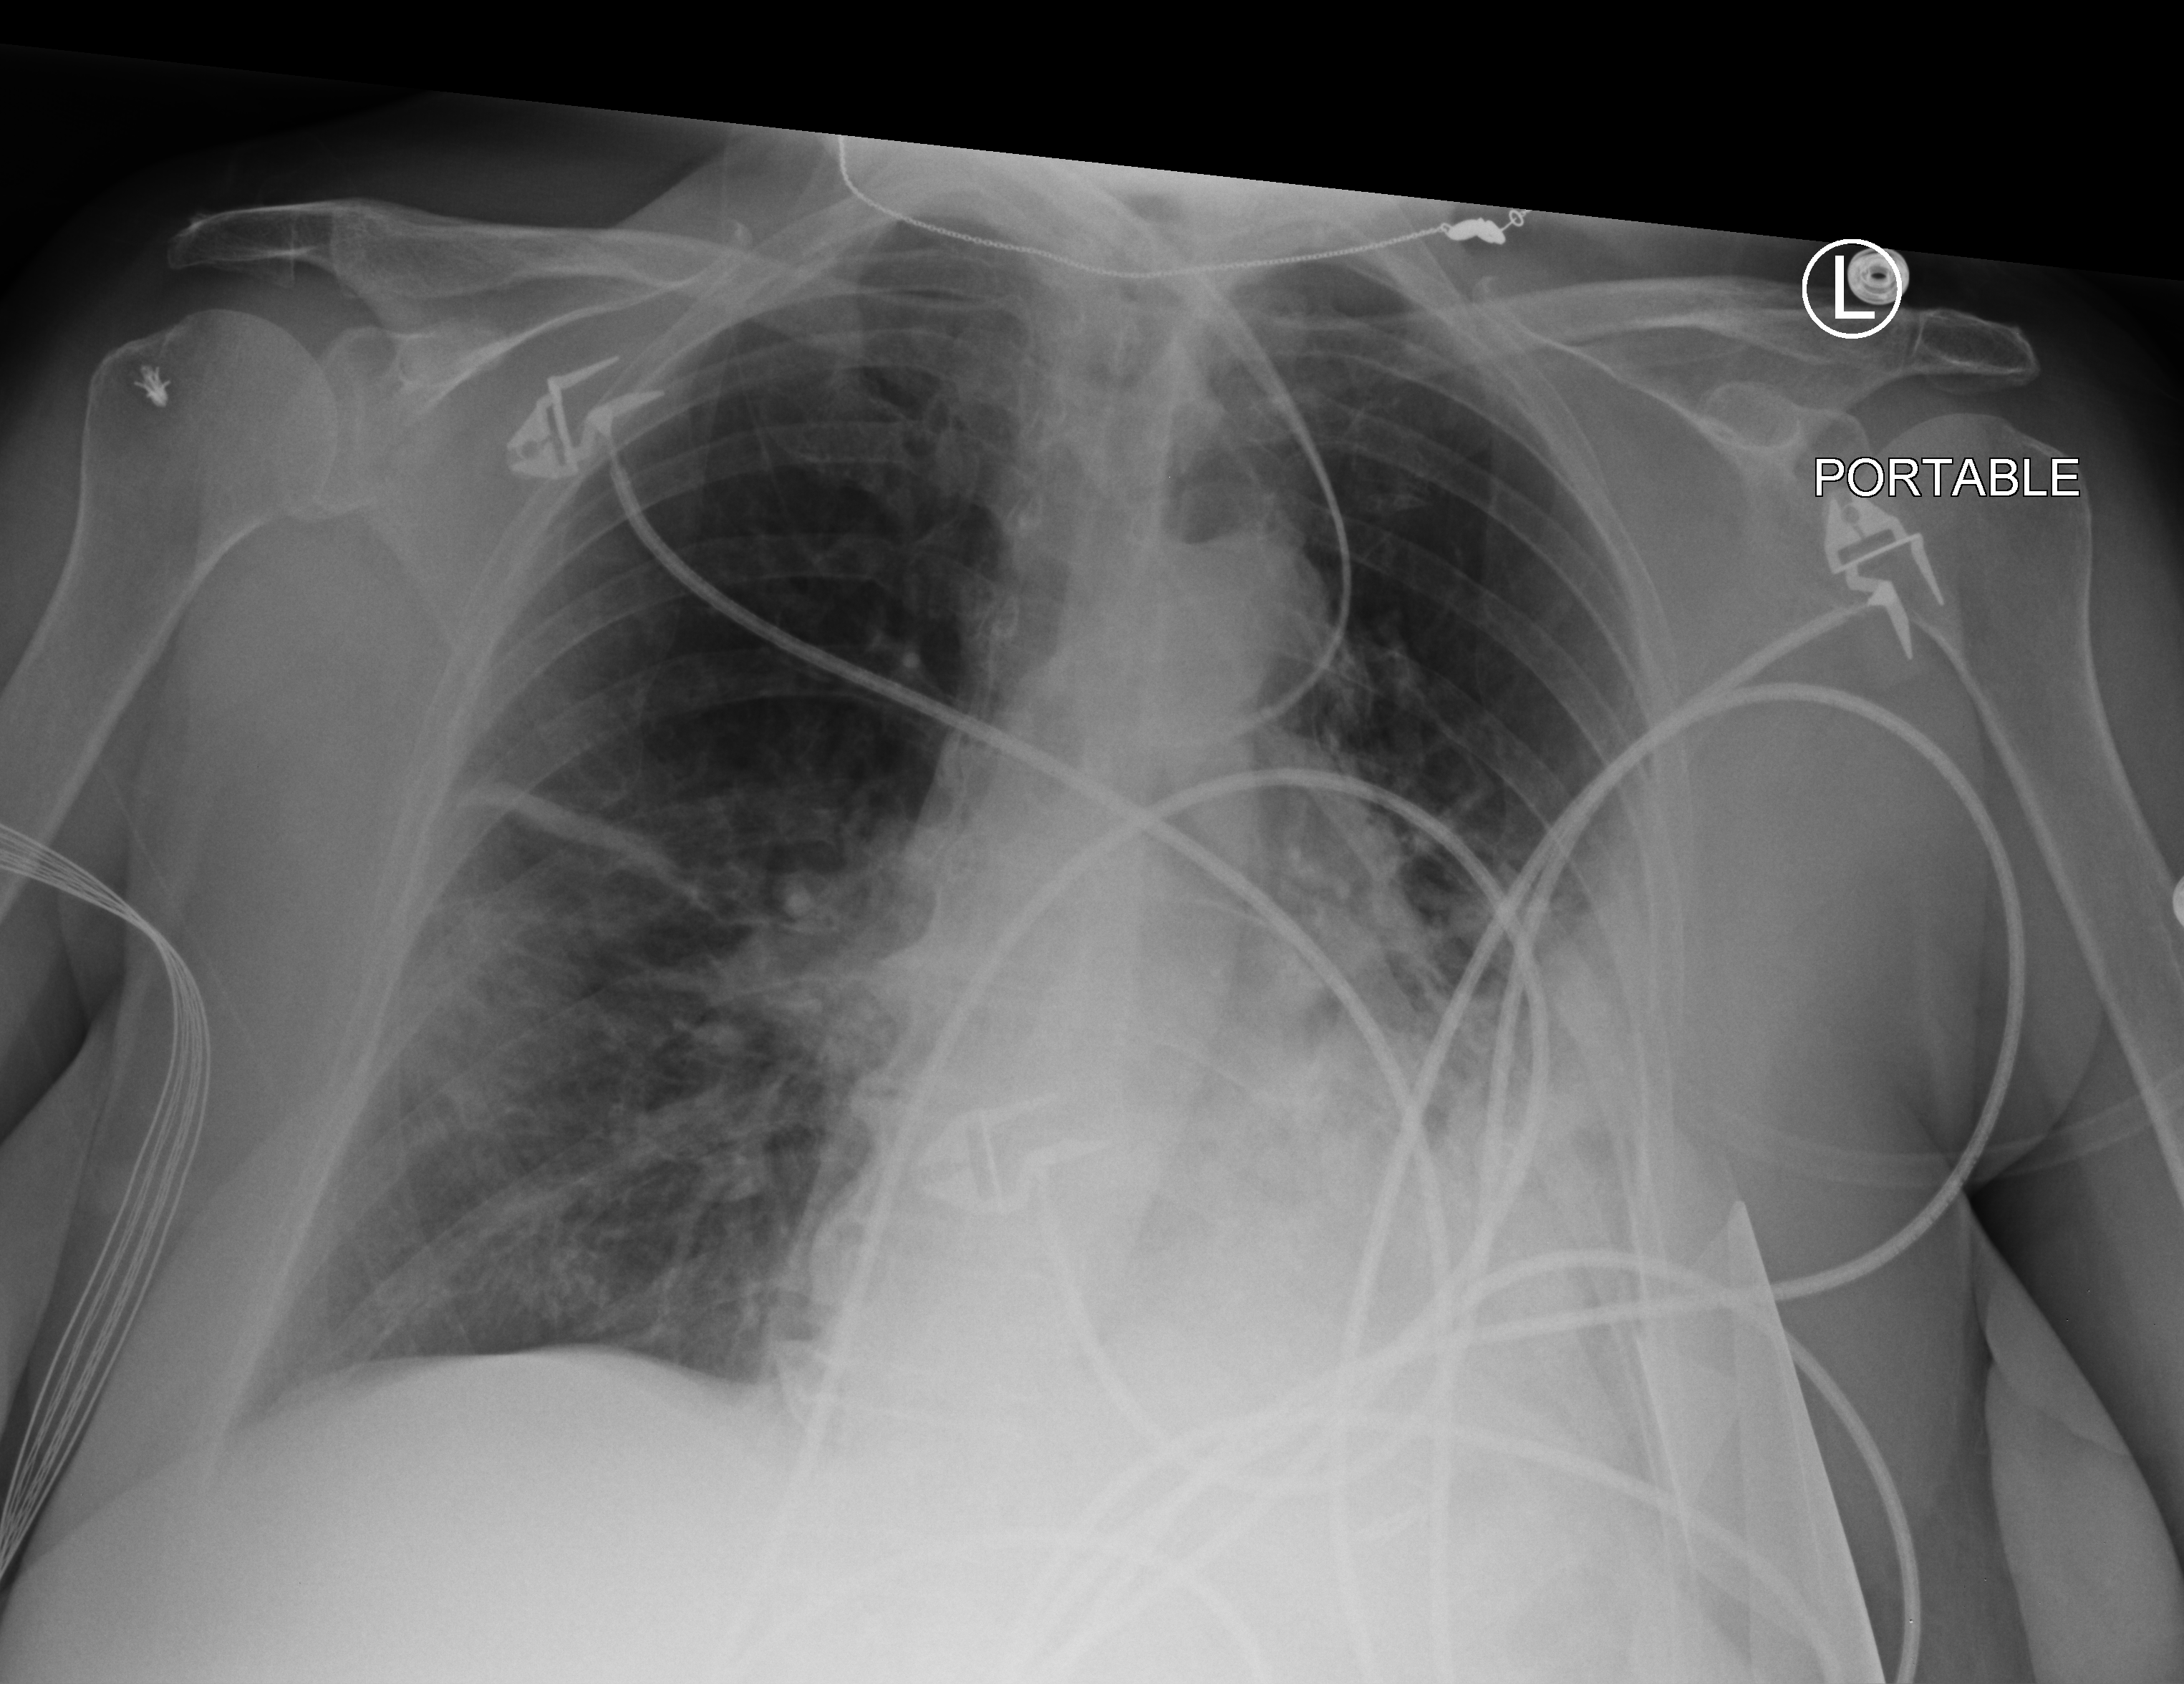
Portable chest radiograph. Patient hospitalised with COVID-19; female, aged 60–74 years.
Hospital-stay facts (about this admission, not read from this image; timing relative to this image not recorded):
- admitted to intensive care during this hospital stay: no
- mechanically ventilated during this hospital stay: no